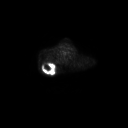
FDG PET of an extremity soft-tissue mass (from a PET/CT study), one axial slice. Slice 218 of 267 in the series (ordered by position). 3.27 mm slice thickness. 128 × 128 image matrix, field of view 700 × 700 mm. Male patient, age 61 years. Case-level facts recorded for this patient, not image findings: histological type: pleiomorphic spindle cell undifferentiated; grade: high; site of the primary tumour: right parascapusular.
Annotated regions visible in this slice (expert contour drawn on MRI and transferred to this co-registered scan by the dataset authors):
- gross tumour volume including surrounding oedema: bounding box [x1, y1, x2, y2] px = [42, 62, 58, 74]
- gross tumour volume (mass): [42, 63, 53, 73]